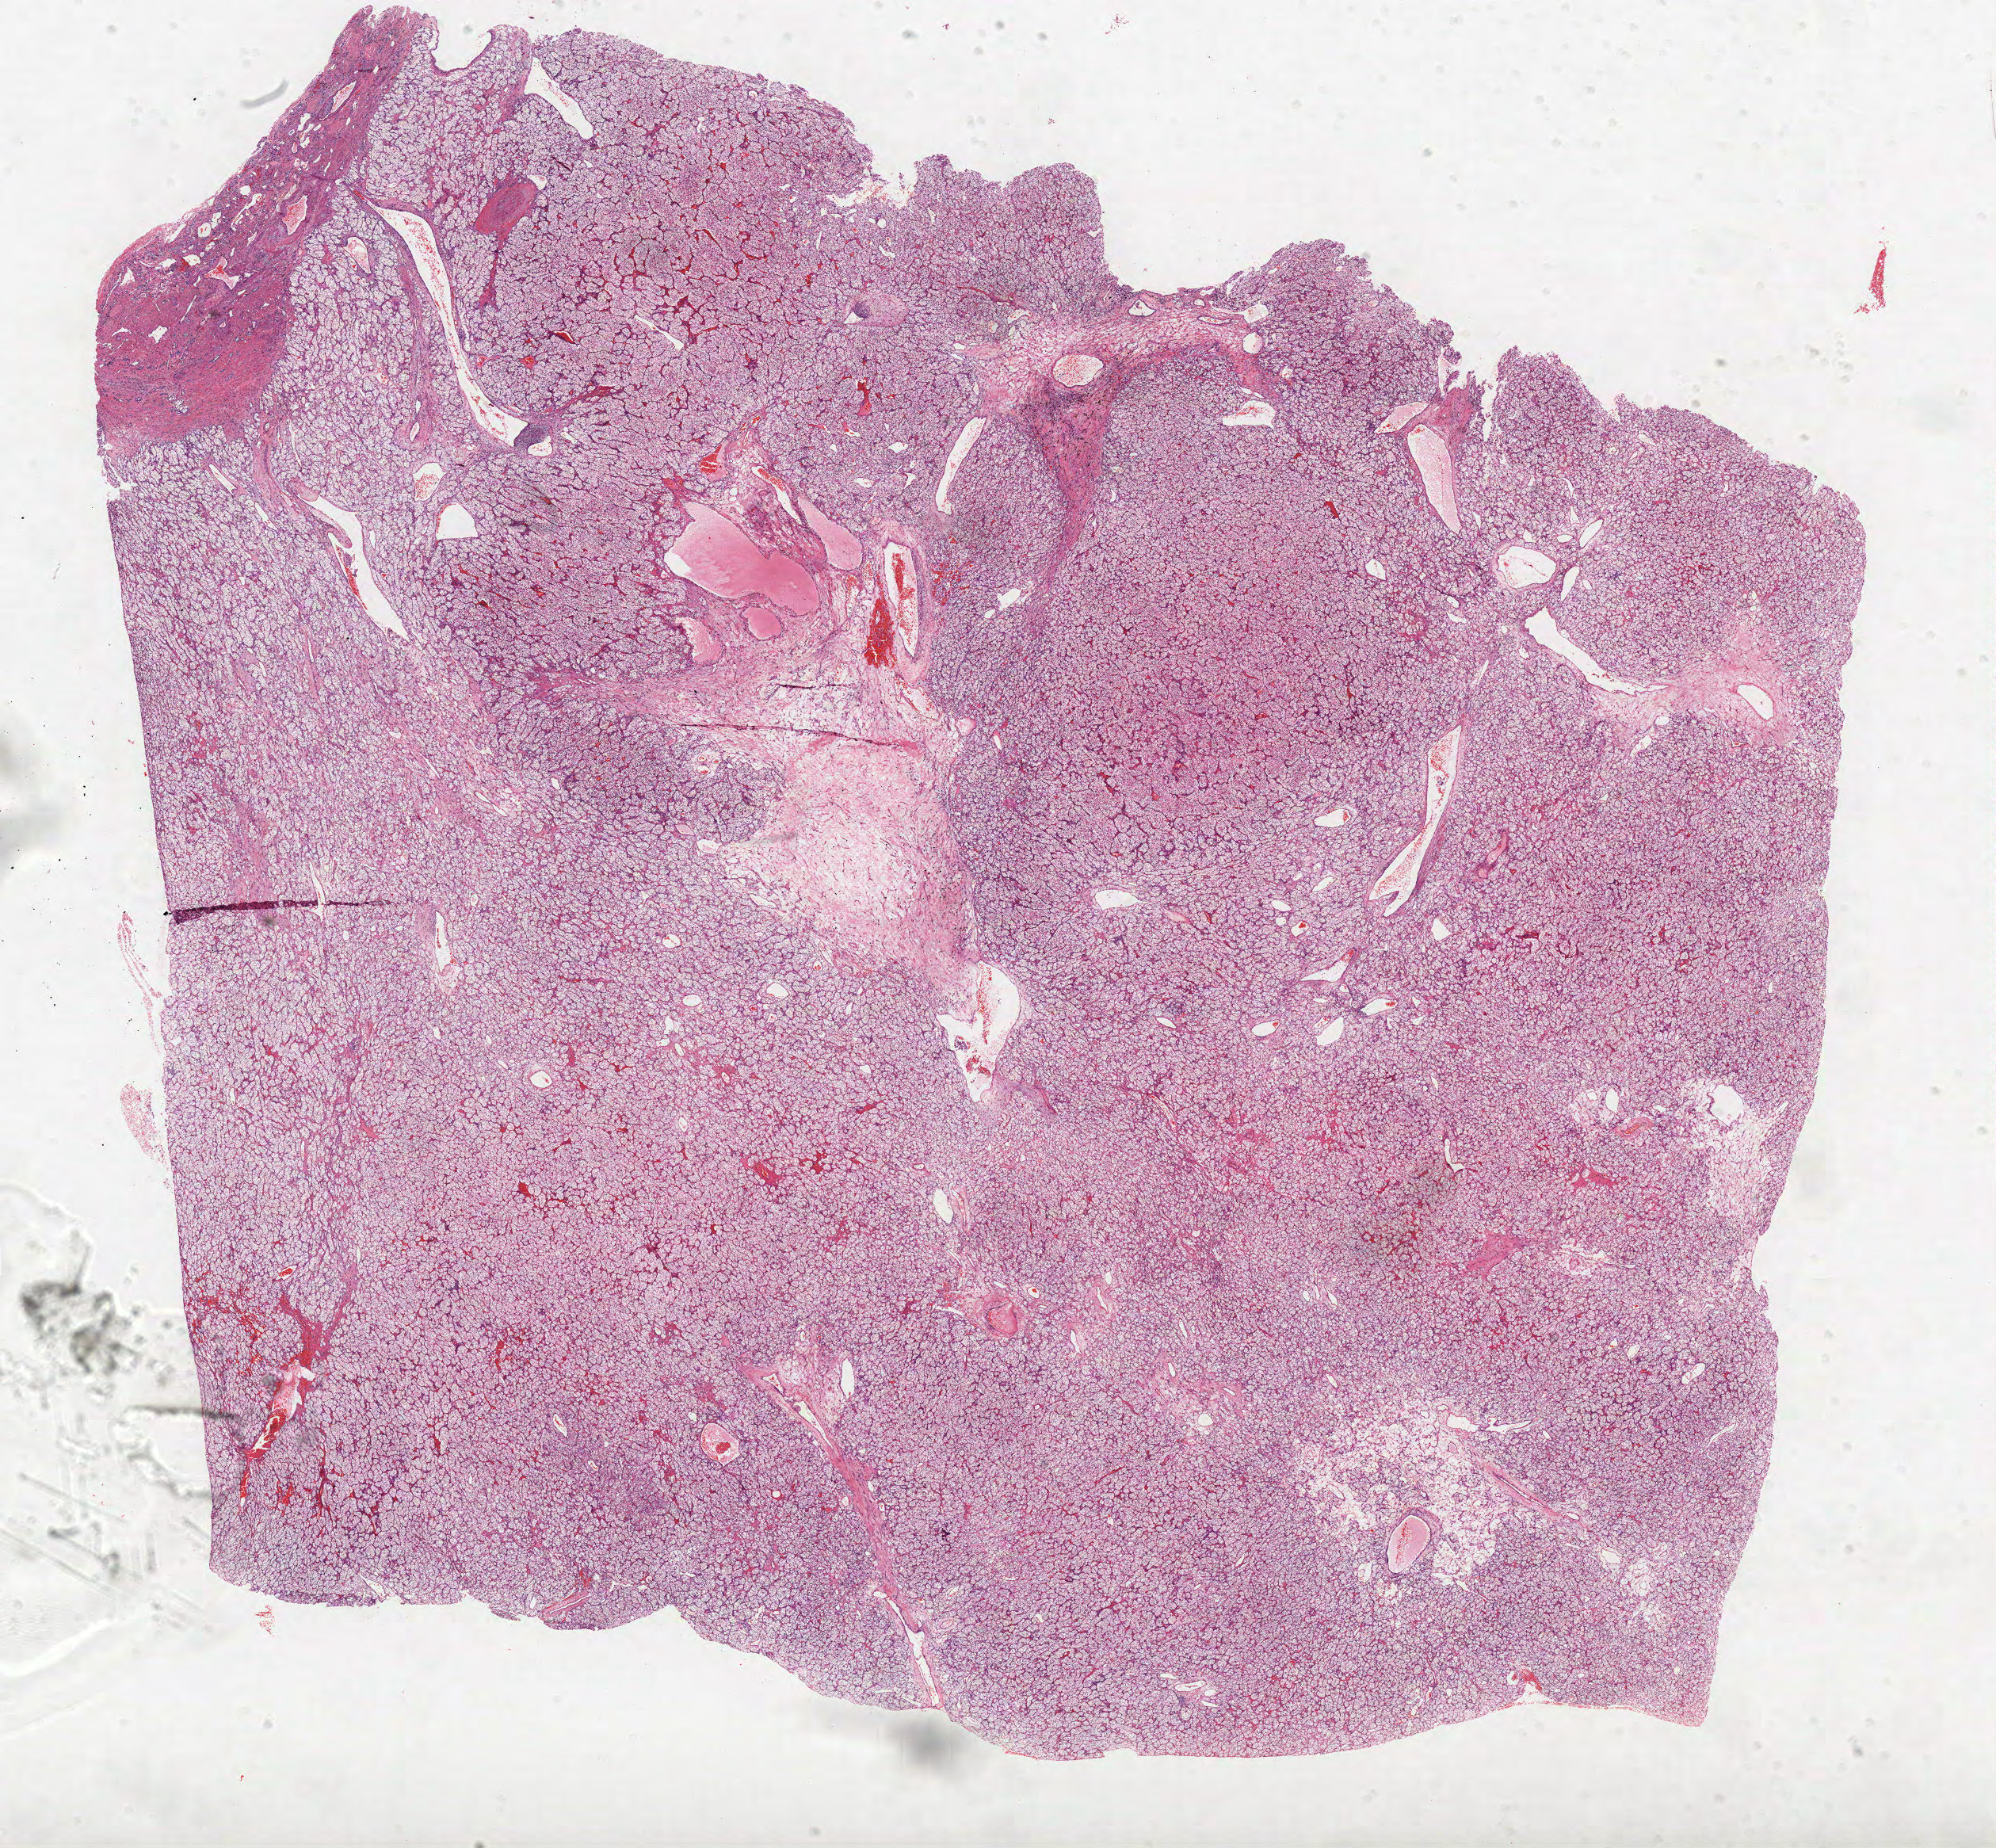
Digitized H&E tissue section (whole slide), shown as a low-resolution overview of the whole scanned area (about 20.1 x 18.6 mm, from a 40x scan). FFPE section. Primary tumour sample from the kidney. Patient: male, age at initial diagnosis 69 years. Histologic grade: G2 (moderately differentiated).
AJCC pathologic stage: I. Diagnosis: Clear cell adenocarcinoma, NOS. Laterality: right. Lymph nodes positive (case pathology): 0 of 5 examined.